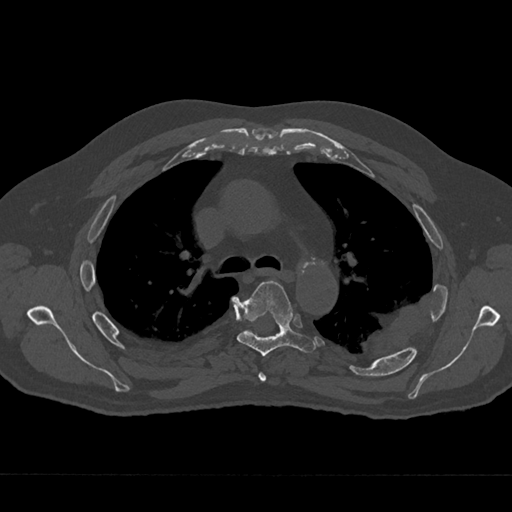
CT including the spine, one axial slice. Slice 475 of 797 in the series (ordered by position). 120 kVp. Bone window (W 1800 / L 400 HU). 0.5 mm slice thickness. 512 × 512 image matrix, field of view 377 × 377 mm. Patient: male, 75 years. From the clinical record (not read from this slice): primary cancer: renal; vertebrae with lytic lesions (as recorded): T4.
Annotated regions visible in this slice (semi-automatic segmentation, software-assisted and operator-edited):
- T4 vertebra: bounding box [x1, y1, x2, y2] px = [258, 372, 266, 382]
- T5 vertebra: [237, 281, 316, 356]
- T6 vertebra: [248, 330, 252, 333]